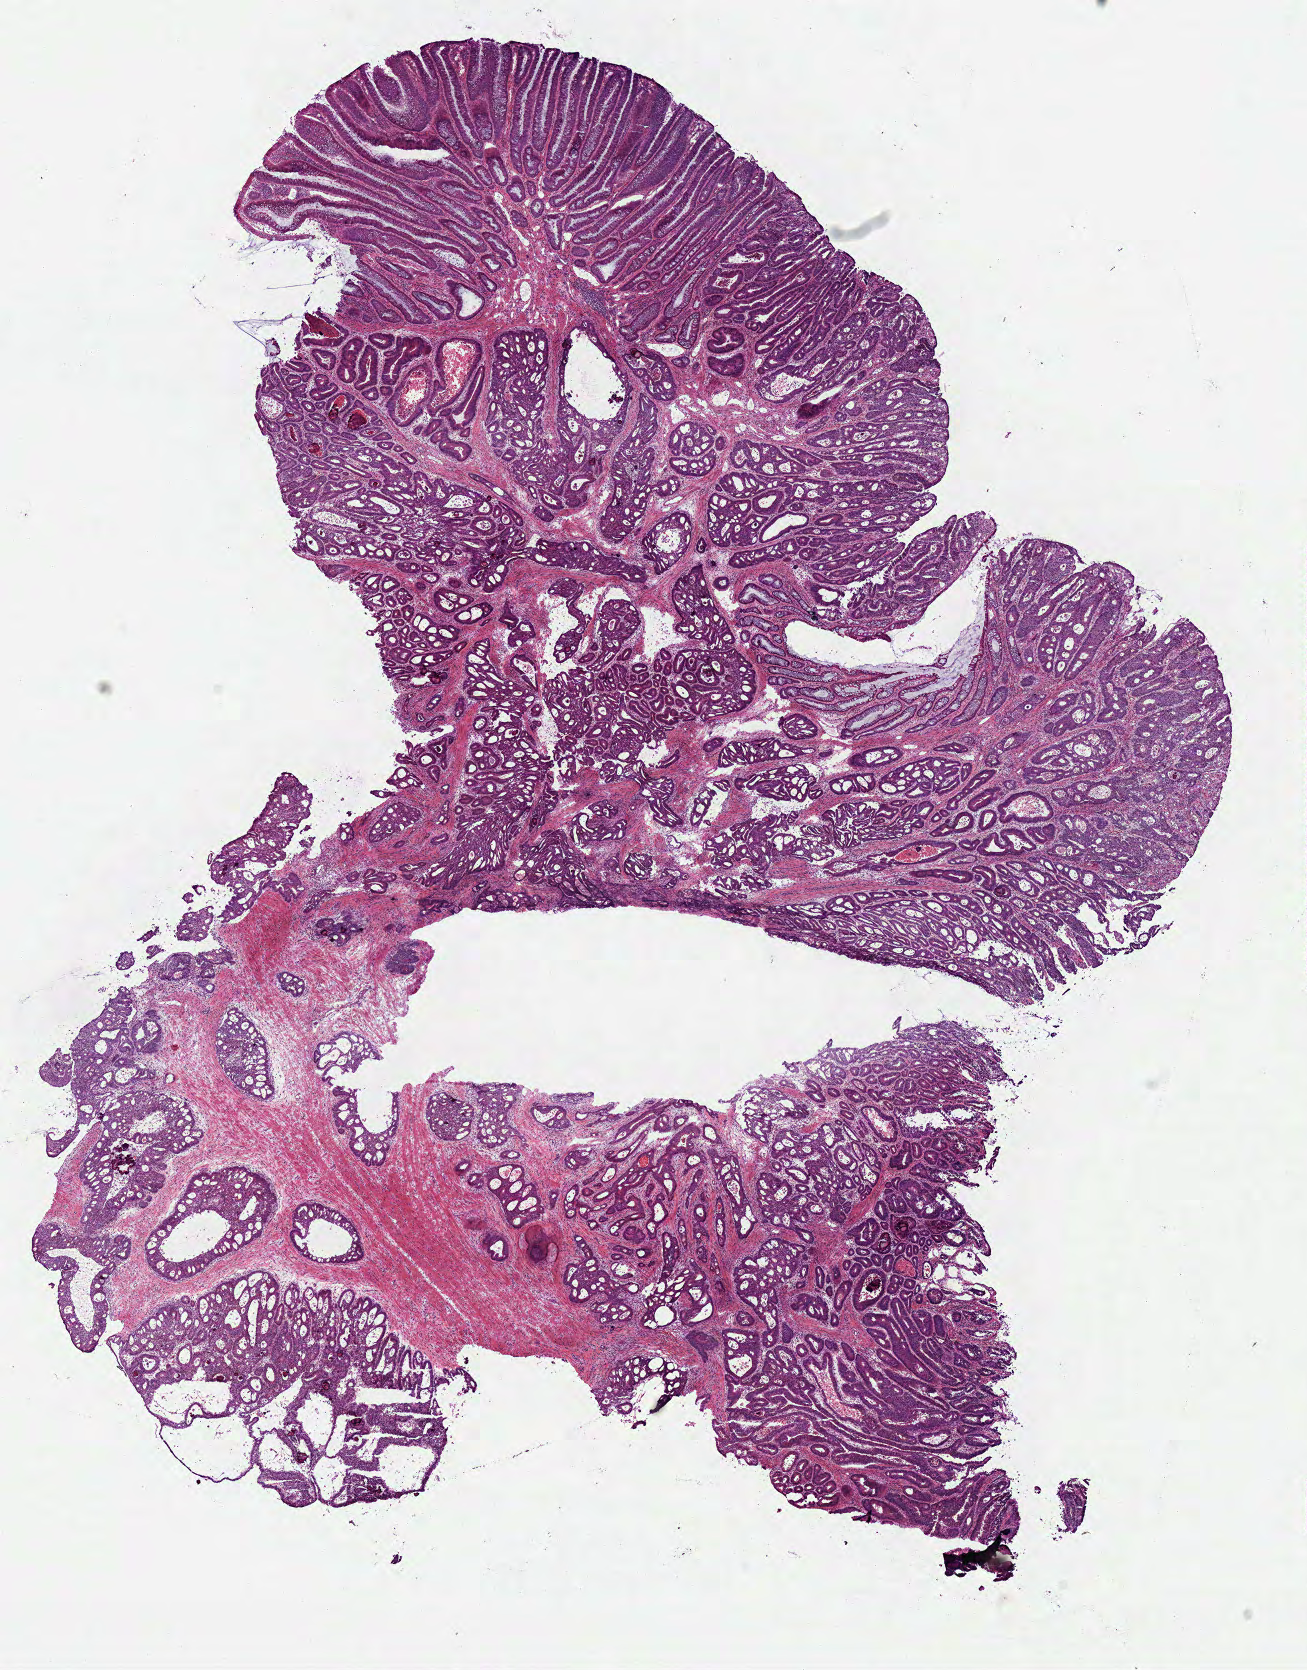
Whole-slide histology image, H&E-stained — low-resolution overview of the scanned area, about 10.3 x 13.1 mm (acquisition: 40x scan), frozen section from the bottom of the tissue portion, primary tumour sample from the colon. Female patient; age at initial diagnosis 70 years. Composition of this section per pathologist review: tumour cells 62%, tumour nuclei 80%, normal cells 15%, stromal cells 15%, necrosis 8%.
Lymph nodes positive (case pathology): 1 of 17 examined. Pathologic diagnosis: Adenocarcinoma, NOS (sigmoid colon). AJCC pathologic stage: IIIB (7th edition).